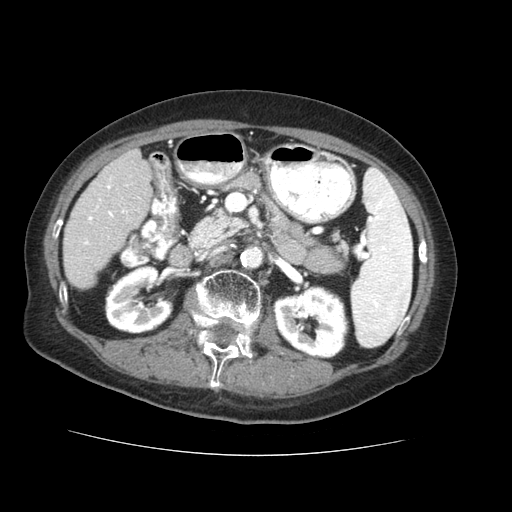
Contrast-enhanced abdominal CT (liver protocol), one axial slice; slice 16 of 73 in the series (ordered by position); 120 kVp; soft-tissue window (W 400 / L 40 HU); 512 × 512 image matrix, field of view 360 × 360 mm. From the clinical record (not read from this slice): diagnosis: hepatocellular carcinoma (patient treated with transarterial chemoembolisation; whether this scan precedes or follows treatment is not stated here); TNM stage (as recorded): Stage-IVB; Child-Pugh class: A; tumour differentiation: well differentiated.
Structures marked on this image (semi-automatic segmentation, software-assisted and operator-edited):
- liver parenchyma outside the tumour (the mass and vessels are separate outlines, so this box may not span the whole liver): bounding box <64,150,150,288> (left, top, right, bottom; pixels)
- liver vessels: <83,176,140,259>